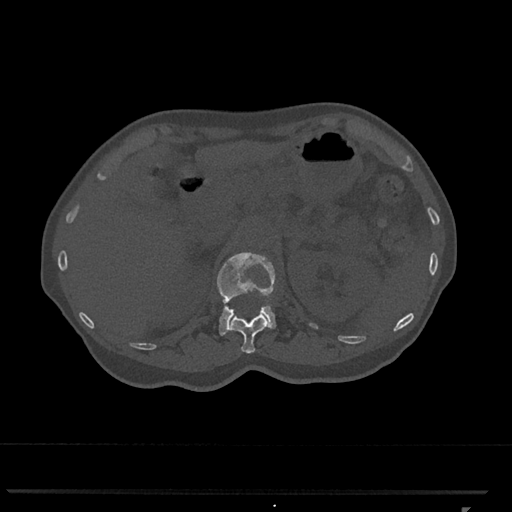
CT including the spine, one axial slice; slice 432 of 793 in the series (ordered by position); reconstruction kernel Br40s/3; 120 kVp; bone window (W 1800 / L 400 HU); 0.5 mm slice thickness; 512 × 512 image matrix, field of view 380 × 380 mm. Female patient, age 62 years. Case-level facts recorded for this patient, not image findings: primary cancer: renal.
Outlined on this slice (semi-automatic segmentation, software-assisted and operator-edited):
- L1 vertebra: box from (x=217, y=252) to (x=276, y=336) px
- T12 vertebra: (x=229, y=313)–(x=268, y=354)